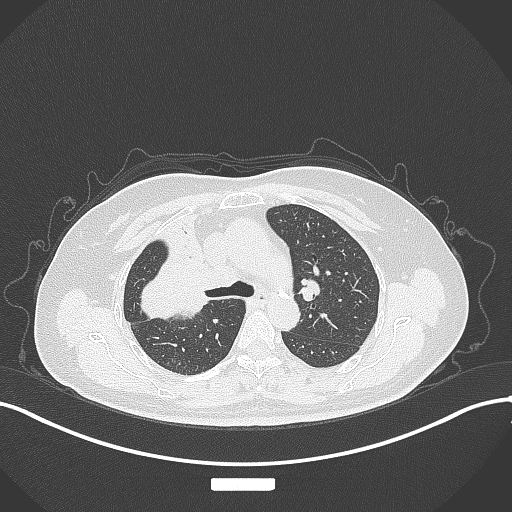
Chest CT, one axial slice; position 213 of 309 along the scan axis; reconstruction kernel B70f; 120 kVp; lung window (W 1500 / L -600 HU); 1 mm slice thickness; 512 × 512 image matrix, field of view 400 × 400 mm. Patient: female, 60 years. From the clinical record (not read from this slice): clinical TNM (as recorded): T3 N1 M1.
Structures marked on this image (rectangle marked by the reading radiologist):
- lung tumour (recorded histology: adenocarcinoma): box from (x=125, y=247) to (x=213, y=325) px